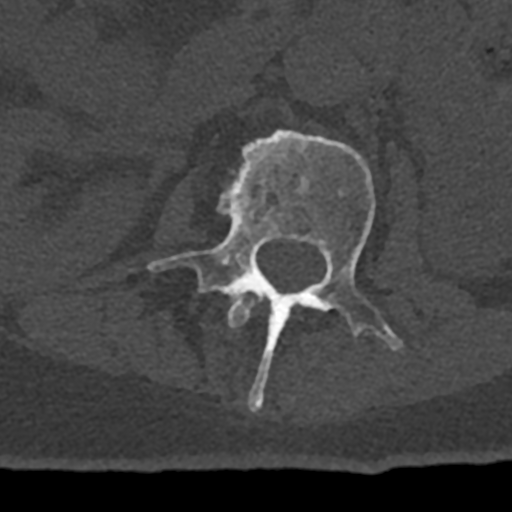
CT including the spine, one axial slice. Slice 385 of 797 in the series (ordered by position). Reconstruction kernel Br40s/3. 120 kVp. Bone window (W 1800 / L 400 HU). 0.5 mm slice thickness. 512 × 512 image matrix, field of view 160 × 160 mm. Male patient, age 74 years. Case-level facts recorded for this patient, not image findings: primary cancer: renal.
Structures marked on this image (semi-automatically segmented with operator editing):
- L1 vertebra: bounding box (x1, y1, x2, y2) in pixels: (227, 291, 257, 328)
- L2 vertebra: (148, 129, 404, 411)